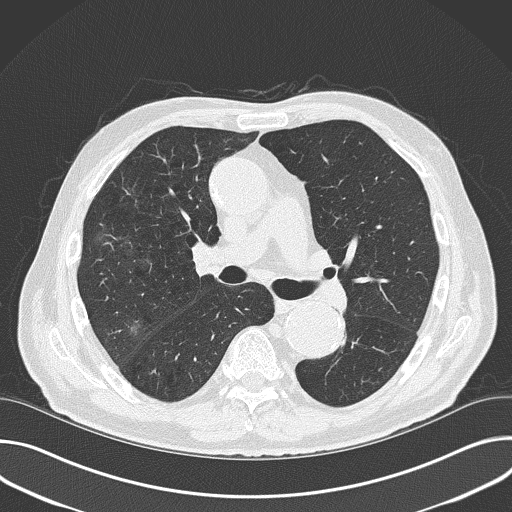
Low-dose screening chest CT, one axial slice; position 97 of 177 along the scan axis; lung window (W 1500 / L -600 HU); 2 mm slice thickness; 512 × 512 image matrix, field of view 380 × 380 mm.
Outlined on this slice (outlined manually by an expert reader):
- lesion 1 (tumor, upper lobe of right lung): bounding box <130,328,138,329> (left, top, right, bottom; pixels)